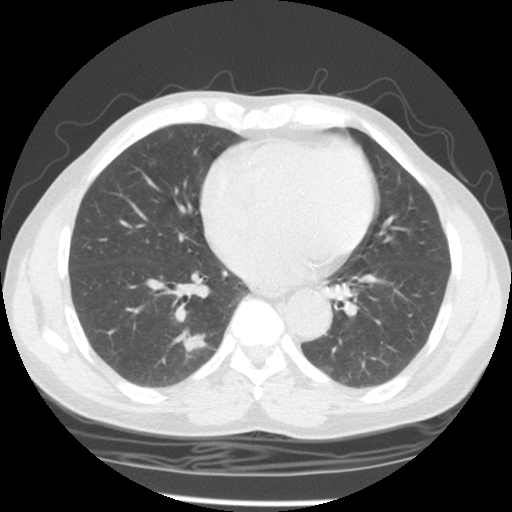
Chest CT (low-dose screening protocol), one axial image, third annual screen, lung window (W 1500 / L -600 HU), 2.5 mm slice thickness, slice 56 of 127 in the series. Male, age 58 years at enrolment.
- Expert-annotated lung lesion, bounding box (x1, y1, x2, y2) in pixels: (168, 327, 215, 362).
- The screening reader recorded 2 non-calcified nodules or masses ≥4 mm on this exam (left upper lobe, right lower lobe); which of them this box marks is not recorded.
- Official screen result: positive, other.
- Lung cancer was diagnosed 323 days after this screen: adenocarcinoma, NOS, right lower lobe, poorly differentiated (G3), stage IIIA (AJCC 6th edition), 15 mm at pathology.